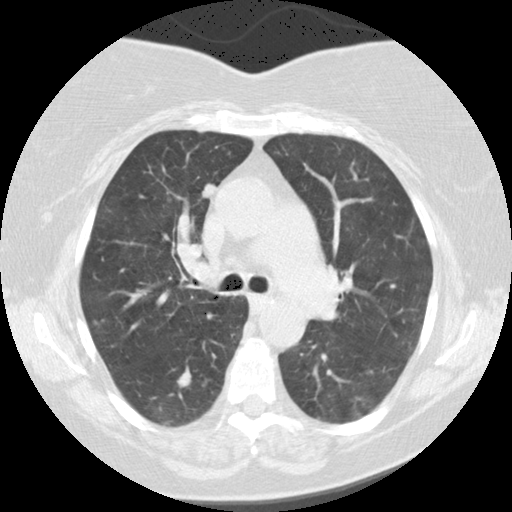
Axial slice from a low-dose chest CT screening exam. Second annual screen. Lung window (W 1500 / L -600 HU). 2.5 mm slice thickness. Female participant, aged 62 years at enrolment.
Lesion marked by an expert reader, bounding box [x1, y1, x2, y2] px = [182, 170, 234, 212]. The screening reader recorded 3 non-calcified nodules or masses ≥4 mm on this exam (right lower lobe, right lower lobe, right lower lobe); which of them this box marks is not recorded. Lung cancer was diagnosed 376 days after this screen (after the third annual screen): adenocarcinoma, NOS, right upper lobe, poorly differentiated (G3), stage IB (AJCC 6th edition), 12 mm at pathology.